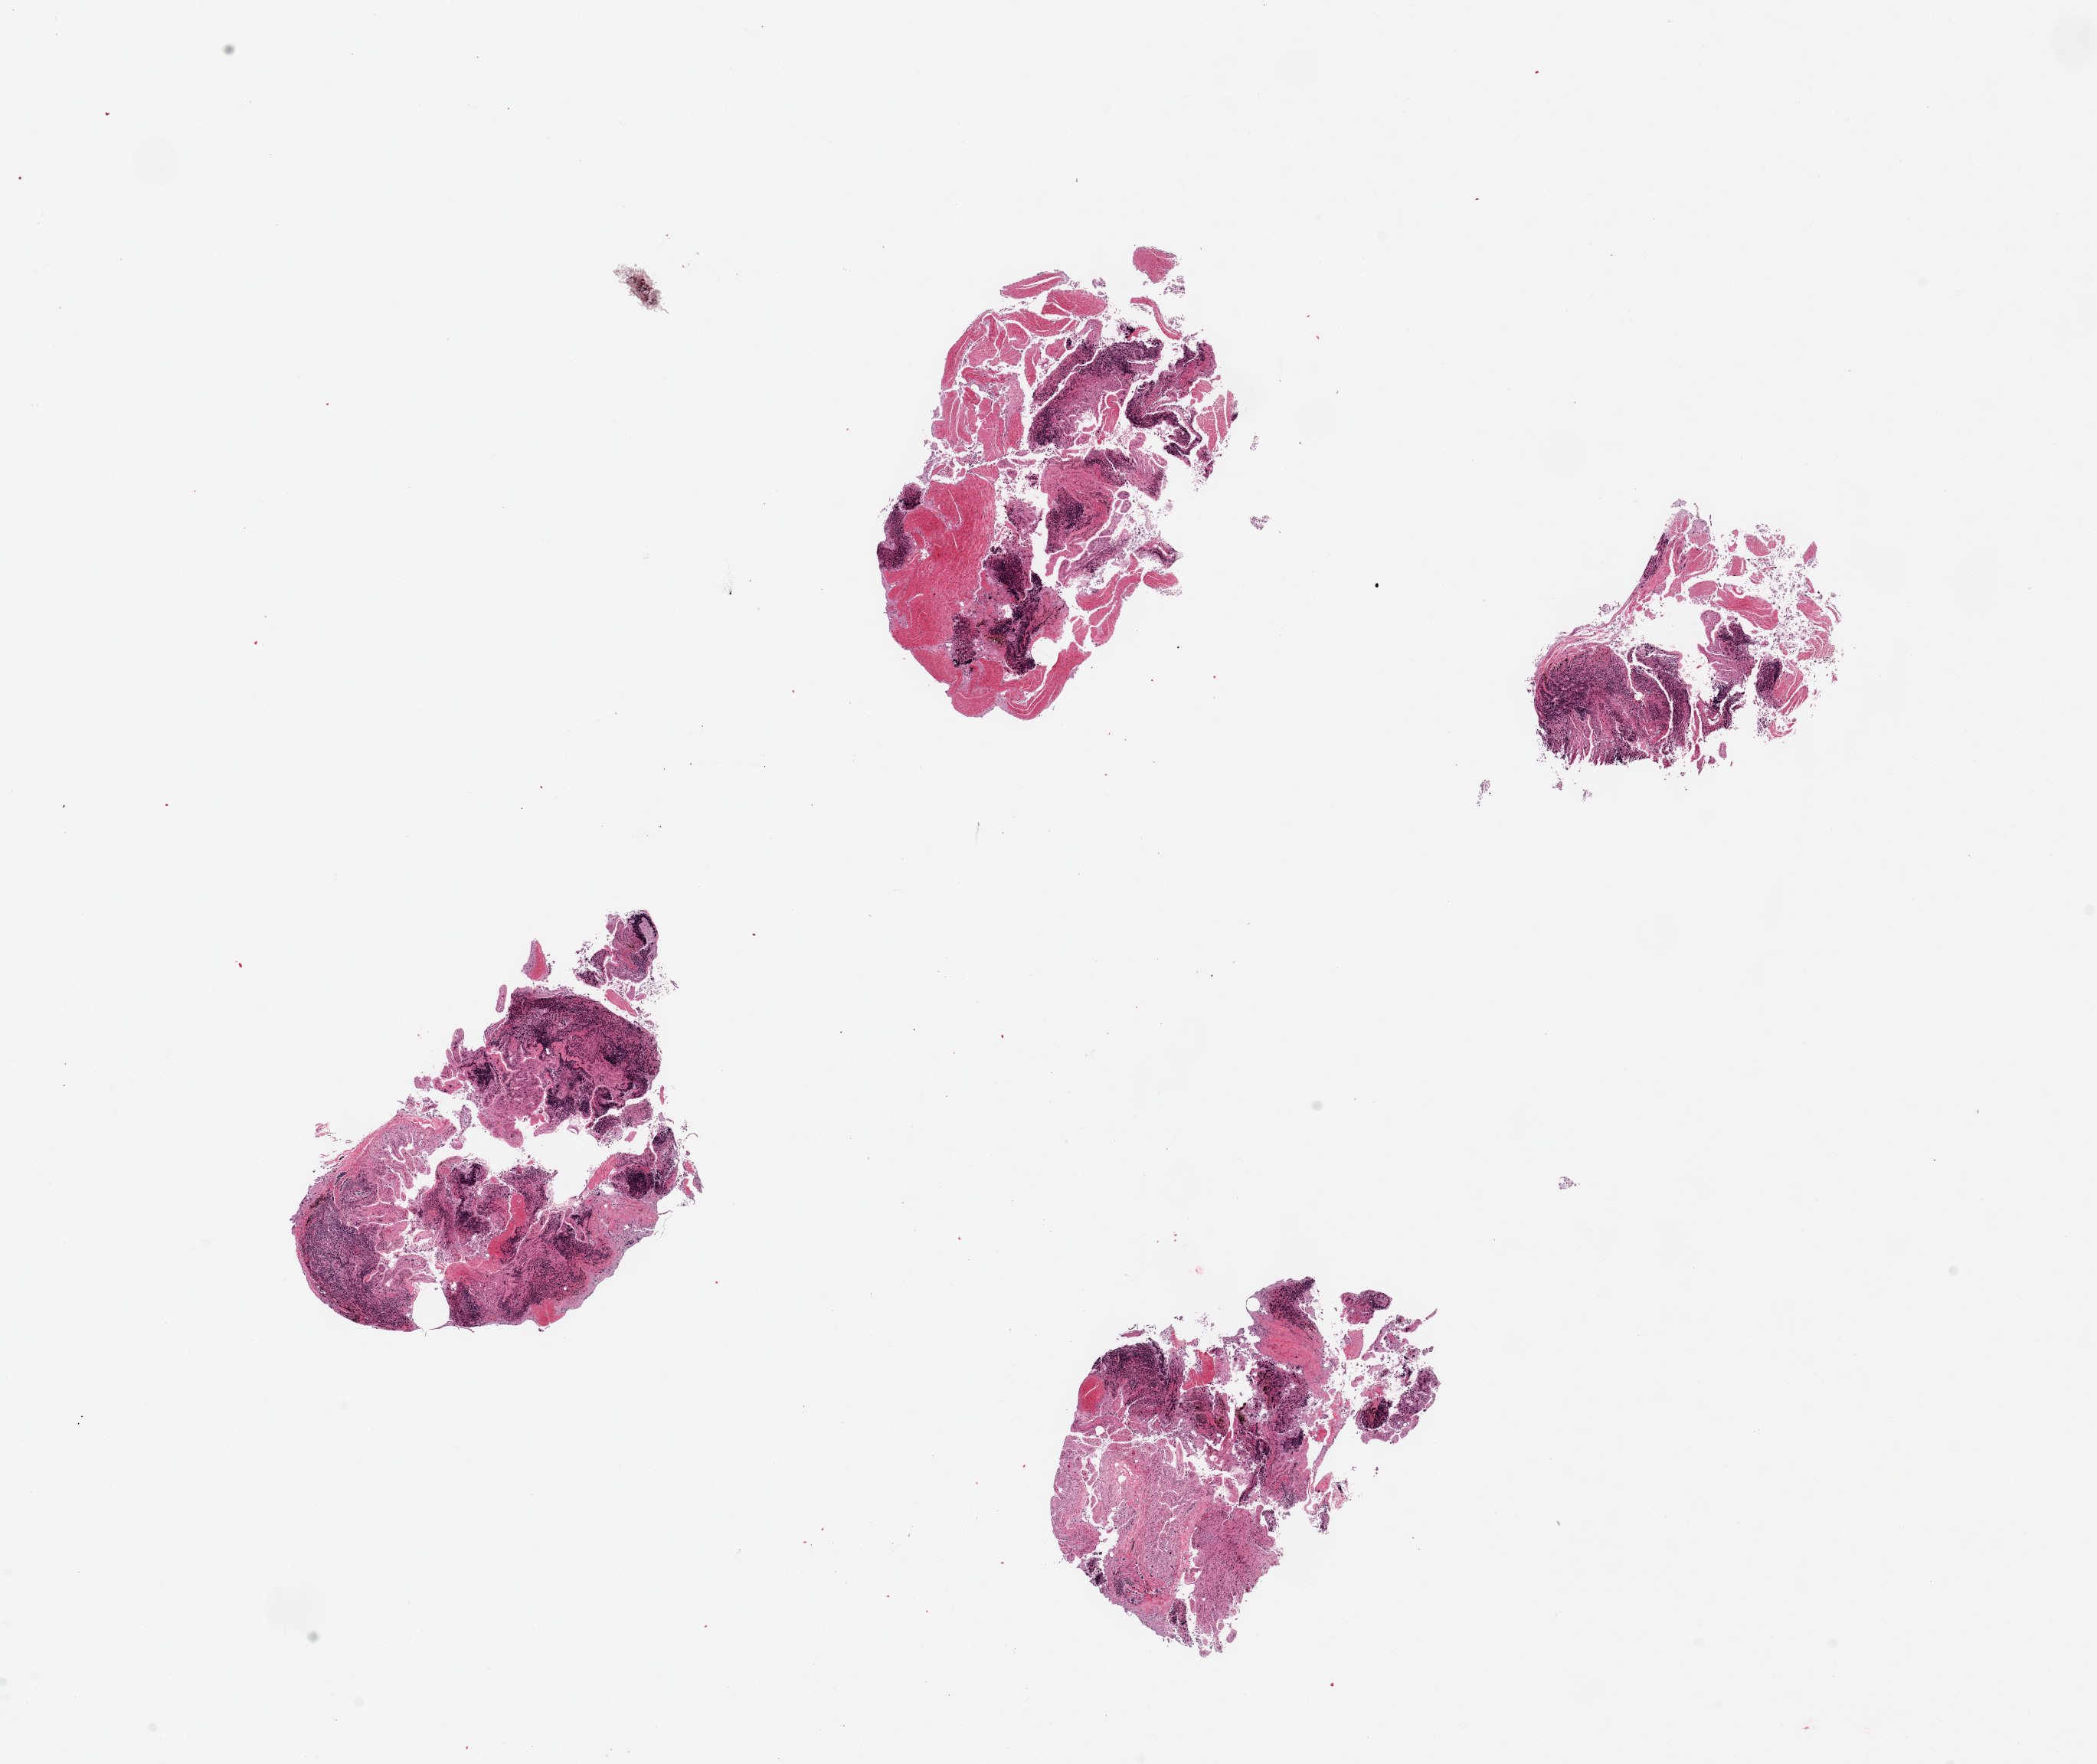
Hematoxylin and eosin (H&E) whole-slide image — whole scanned area (about 21.7 x 18.2 mm) shown as a low-resolution overview; PAXgene-fixed, paraffin-embedded tissue; section of ileum (target tissue); tissue donor sample.
Pathologist's review note for this sample: 4 pieces, up to 5x4mm; Good dissection: multiple lymphoid nodules despite mucosal autolysis.